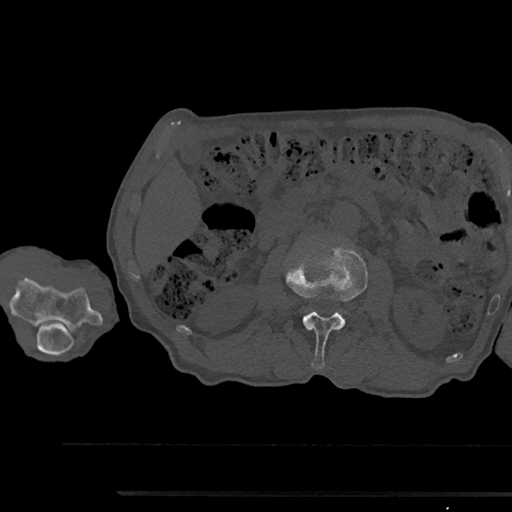
CT including the spine, one axial slice. Reconstruction kernel Br40s/3. 120 kVp. Bone window (W 1800 / L 400 HU). 0.5 mm slice thickness. 512 × 512 image matrix, field of view 367 × 367 mm. Patient: male, 79 years. From the clinical record (not read from this slice): primary cancer: prostate.
Structures marked on this image (semi-automatic segmentation, software-assisted and operator-edited):
- L2 vertebra: box from (x=286, y=246) to (x=367, y=369) px